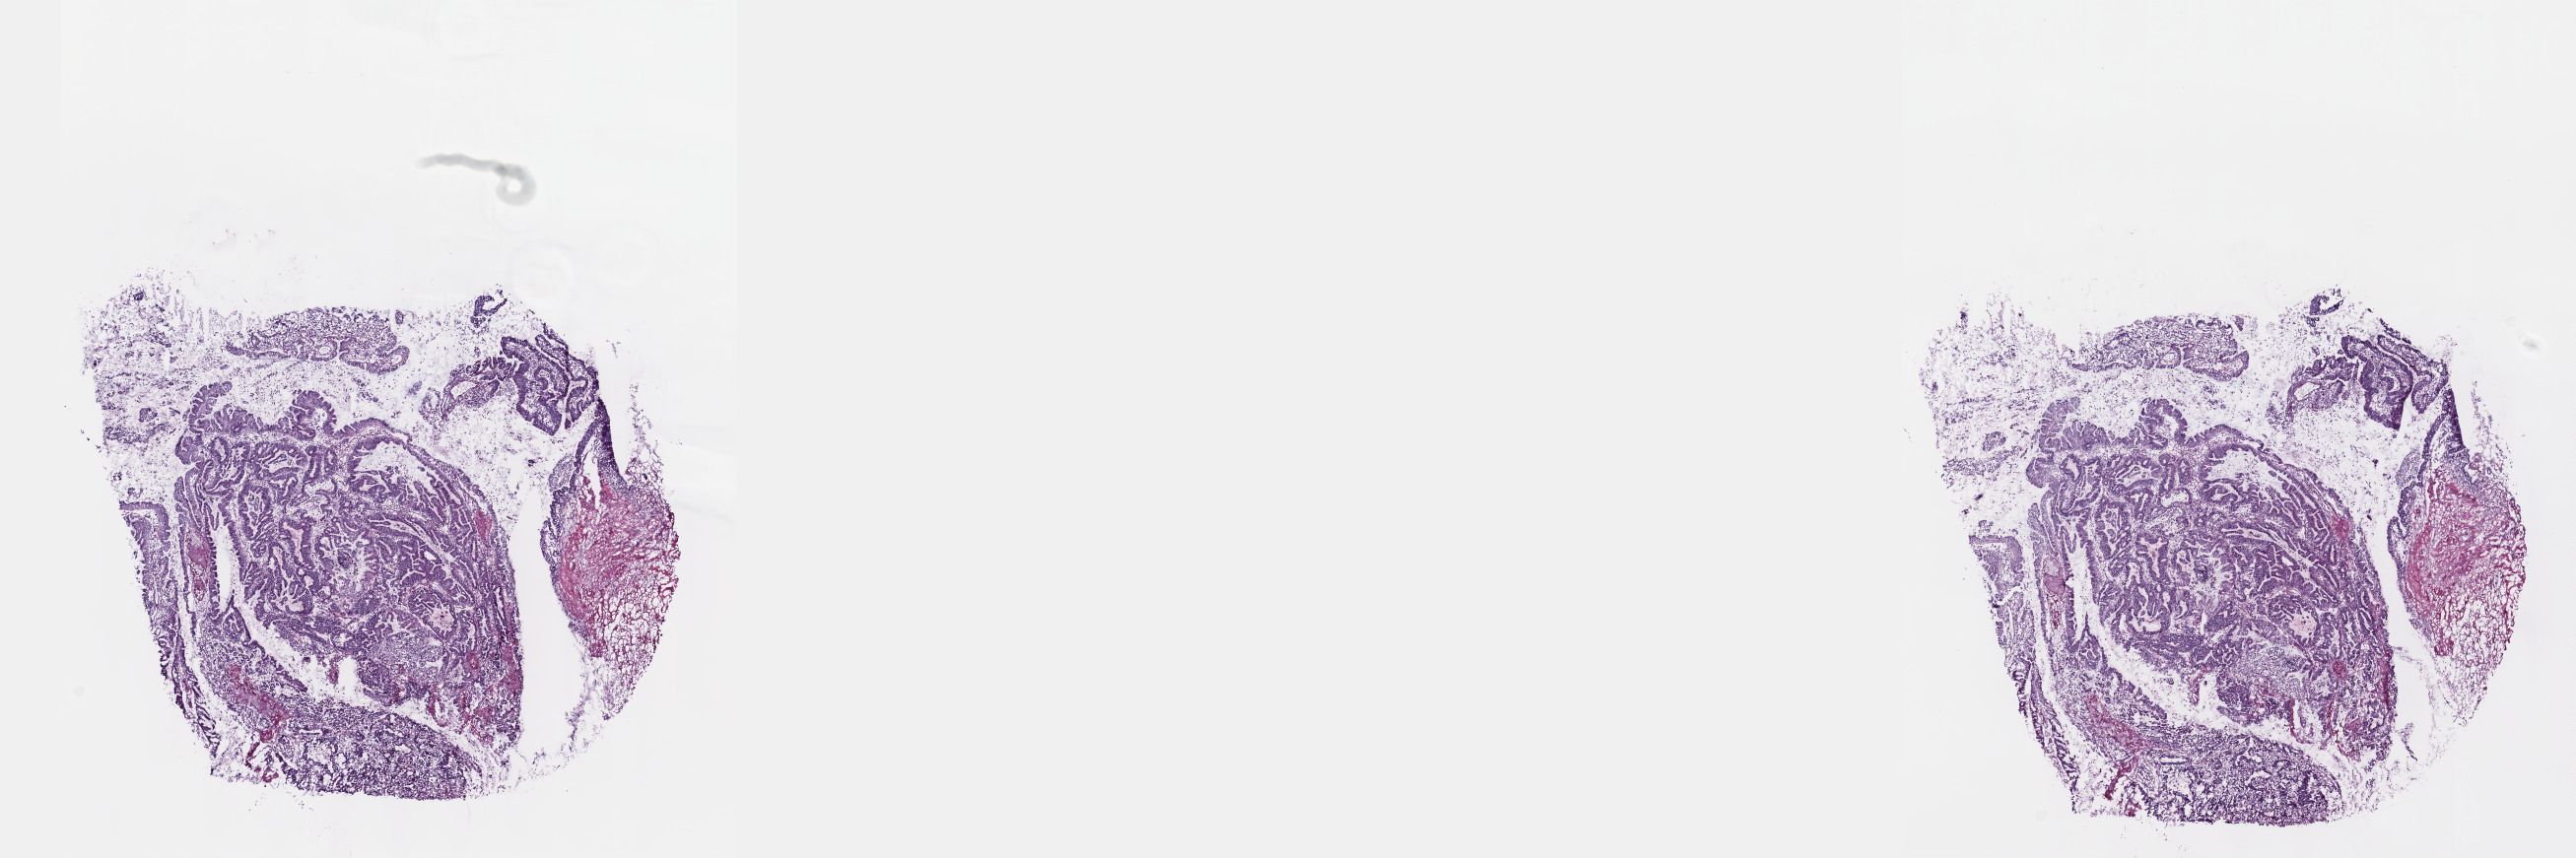
Hematoxylin and eosin (H&E) stained whole-slide image, whole scanned area (about 21.1 x 7.0 mm) shown as a low-resolution overview, frozen section, stomach, primary tumour sample. Female, age 72 years at initial diagnosis. Slide review estimates, as recorded: tumour cells 100%, tumour nuclei 65%.
Histologic diagnosis: Tubular adenocarcinoma.